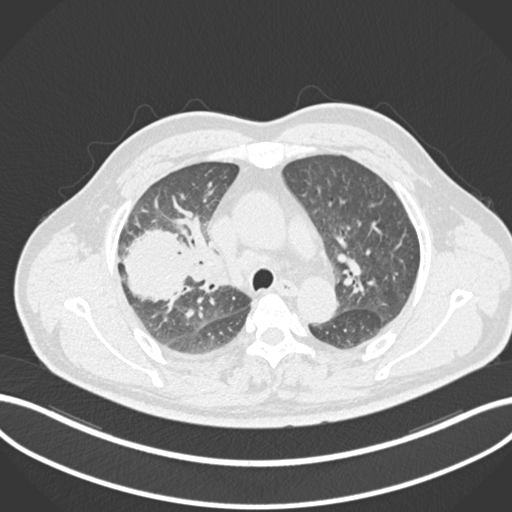
Chest CT, one axial slice; position 658 of 852 along the scan axis; reconstruction kernel B30f; 120 kVp; lung window (W 1500 / L -600 HU); 1 mm slice thickness; 512 × 512 image matrix. Patient: male, 55 years. From the clinical record (not read from this slice): clinical TNM (as recorded): T3 N2 M1.
Structures marked on this image (rectangle marked by the reading radiologist):
- lung tumour (recorded histology: adenocarcinoma): bounding box <116,225,194,303> (left, top, right, bottom; pixels)